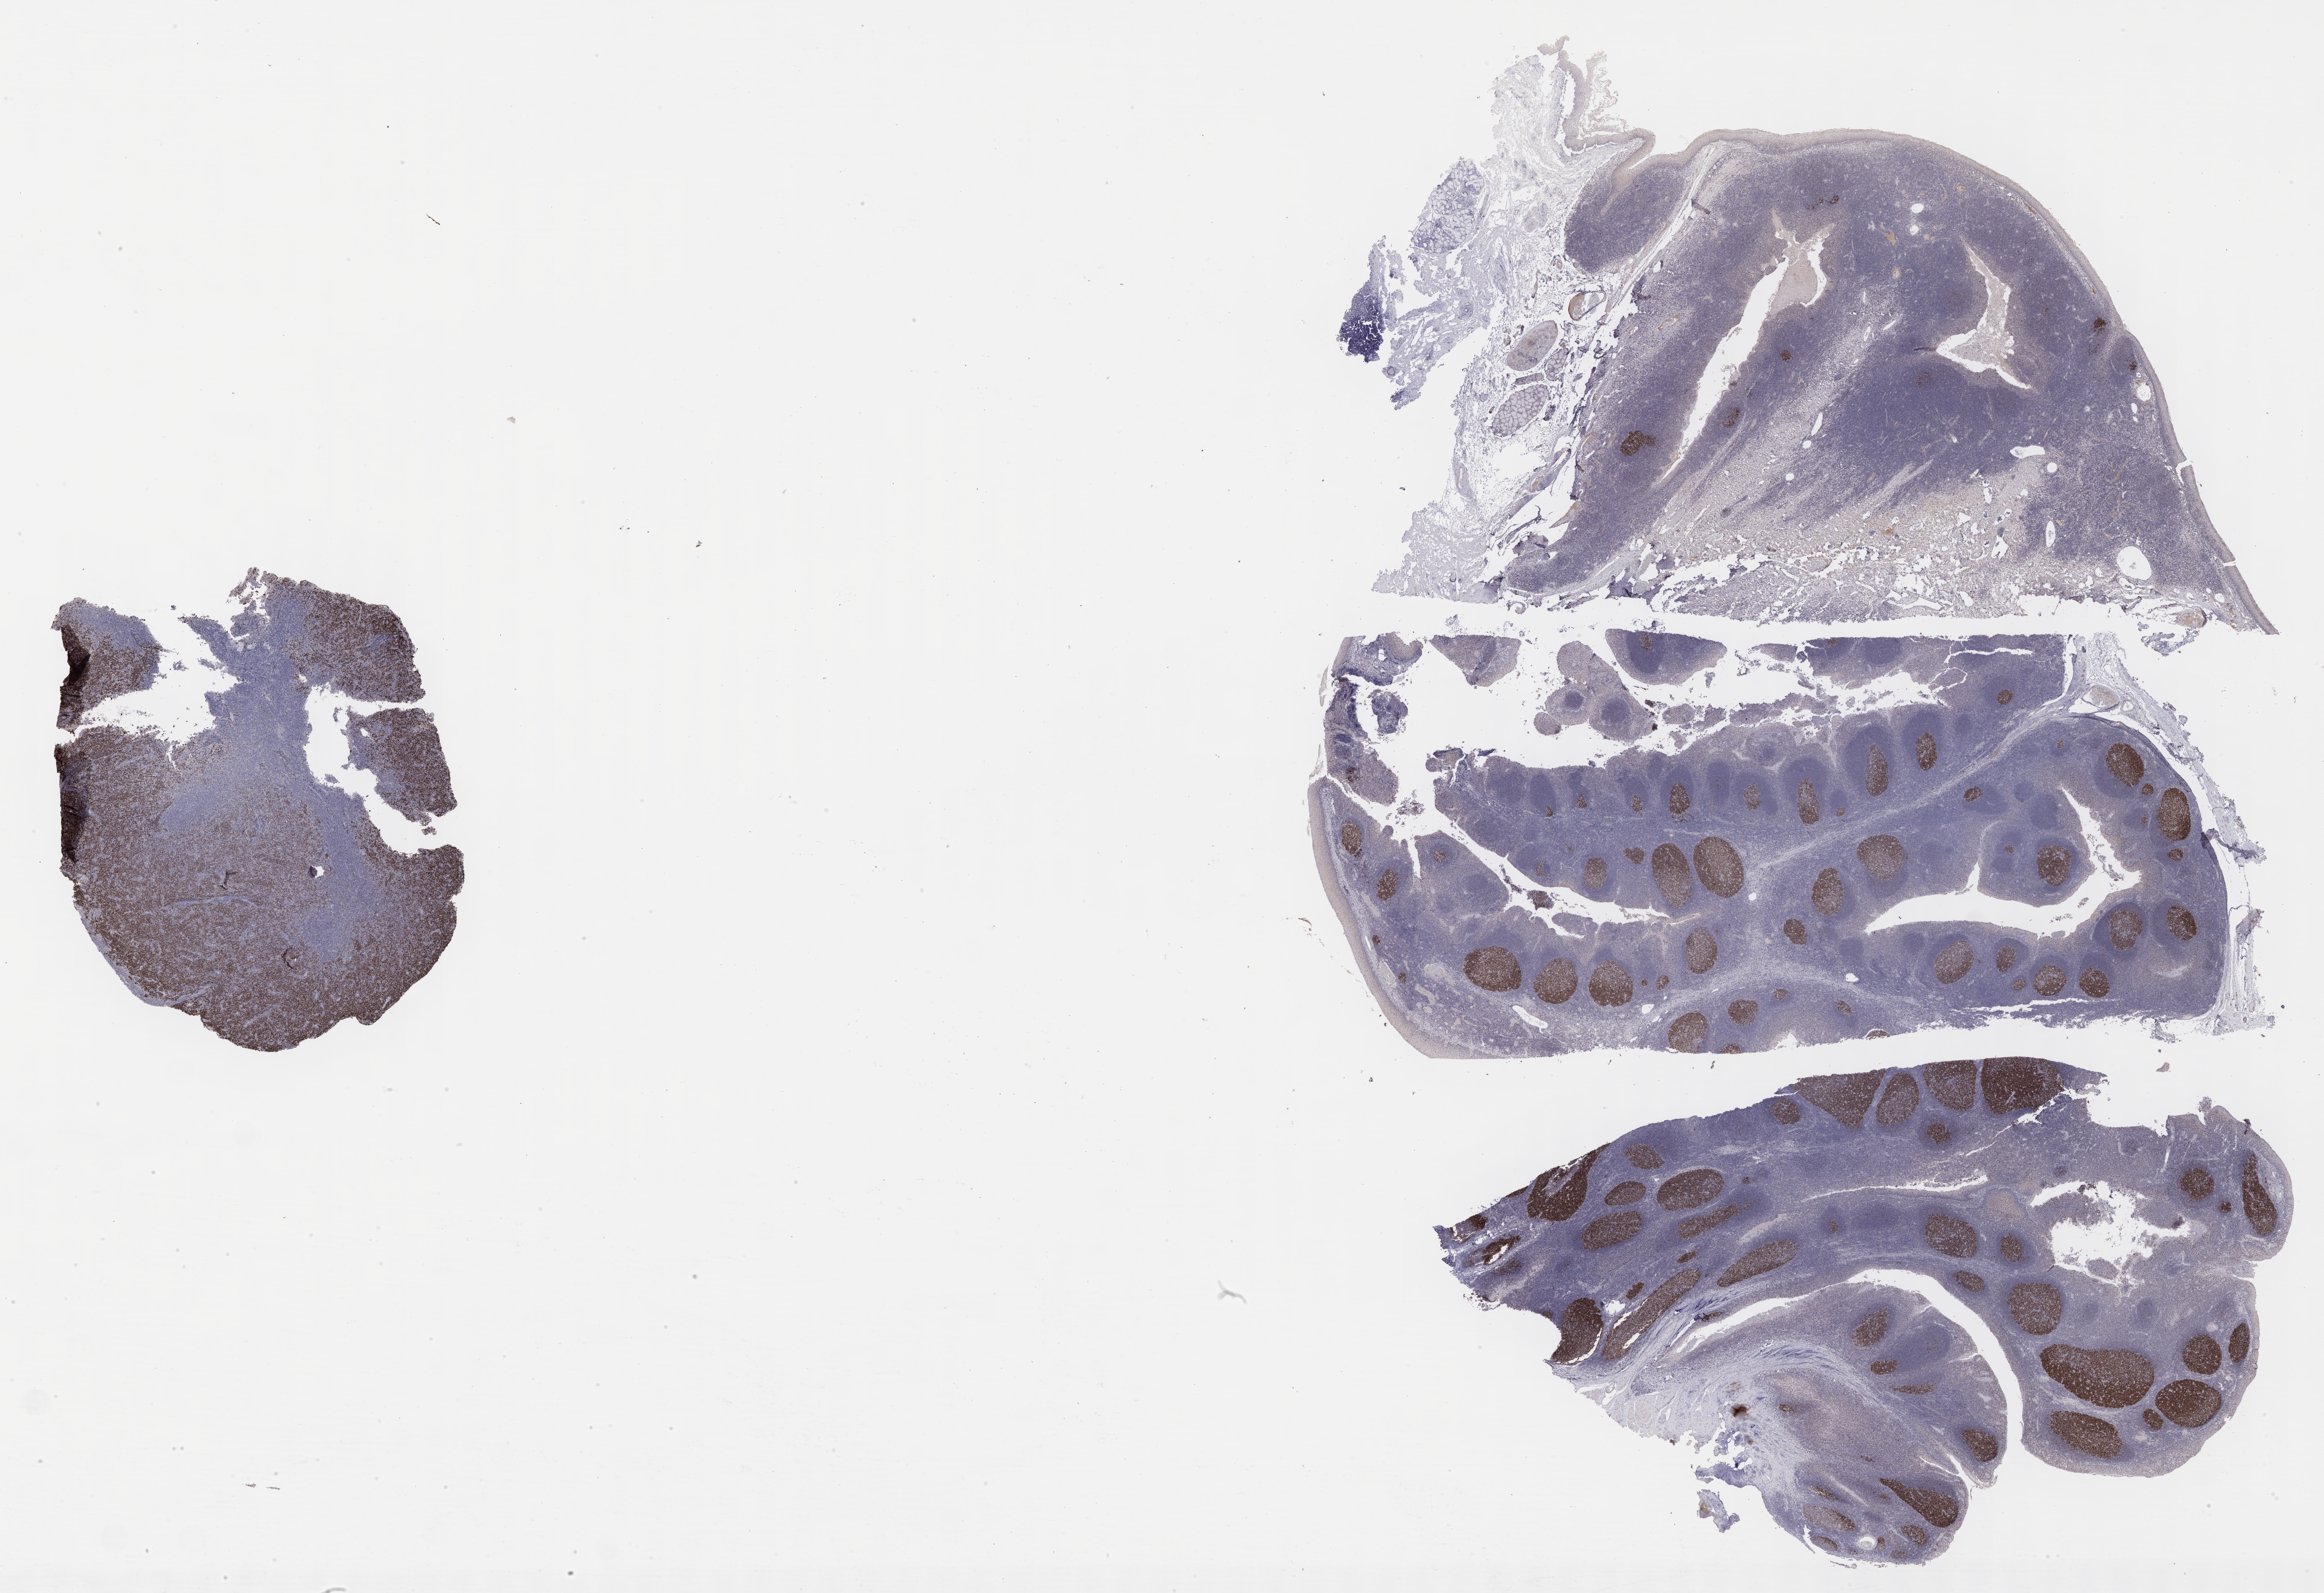
Whole-slide image, immunohistochemical stain for BCL6 — a low-resolution overview of the entire scanned area, about 31.7 x 21.7 mm; tumor tissue; site: liver. Patient: male, age 46 years.
Histologic diagnosis: Diffuse large B-cell lymphoma, NOS.